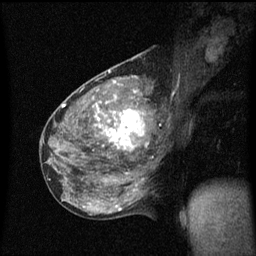
Breast MRI (dynamic contrast-enhanced), one sagittal slice; position 28 of 60 along the scan axis; dynamic contrast-enhanced series, image 2 of 3 at this slice position (ordered by acquisition); 1.5 T; TE 4.2 ms, TR 8.4 ms; 2 mm slice thickness; 256 × 256 image matrix, field of view 200 × 200 mm. Female patient, age 49 years.
Structures marked on this image (semi-automatically segmented with operator editing):
- analysis volume of interest (the breast-tissue region the enhancement analysis was run in; not a lesion): bounding box <103,90,157,151> (left, top, right, bottom; pixels)
- tumour enhancement mask (voxels above the 70 % enhancement threshold inside the analysis volume of interest): <105,90,149,149>